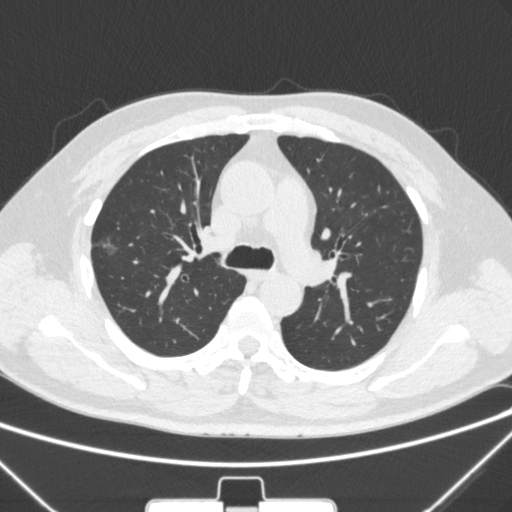
Chest CT, one axial slice; slice 204 of 320 in the series (ordered by position); 120 kVp; lung window (W 1500 / L -600 HU); 1 mm slice thickness; 512 × 512 image matrix, field of view 350 × 350 mm. Male patient, age 58 years. From the clinical record (not read from this slice): clinical TNM (as recorded): T1c N0 M0.
Structures marked on this image (bounding box drawn by a radiologist):
- lung tumour (recorded histology: adenocarcinoma): bounding box [x1, y1, x2, y2] px = [90, 232, 127, 265]